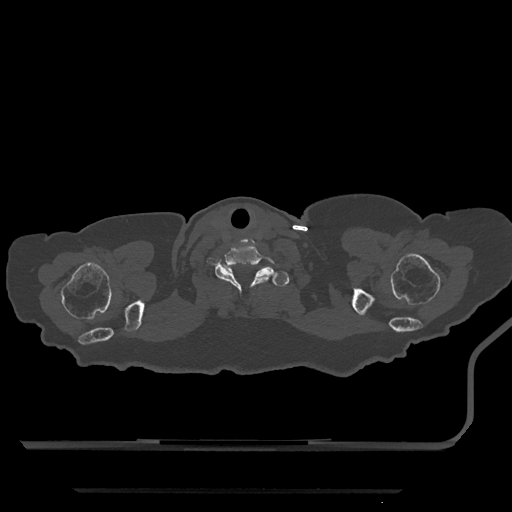
CT including the spine, one axial slice. Position 732 of 797 along the scan axis. Bone window (W 1800 / L 400 HU). 512 × 512 image matrix, field of view 440 × 440 mm. Patient: female, 51 years. Case-level facts recorded for this patient, not image findings: primary cancer: neuro; vertebrae with lytic lesions (as recorded): T8.
Outlined on this slice (semi-automatically segmented with operator editing):
- T1 vertebra: bounding box <223,265,290,287> (left, top, right, bottom; pixels)